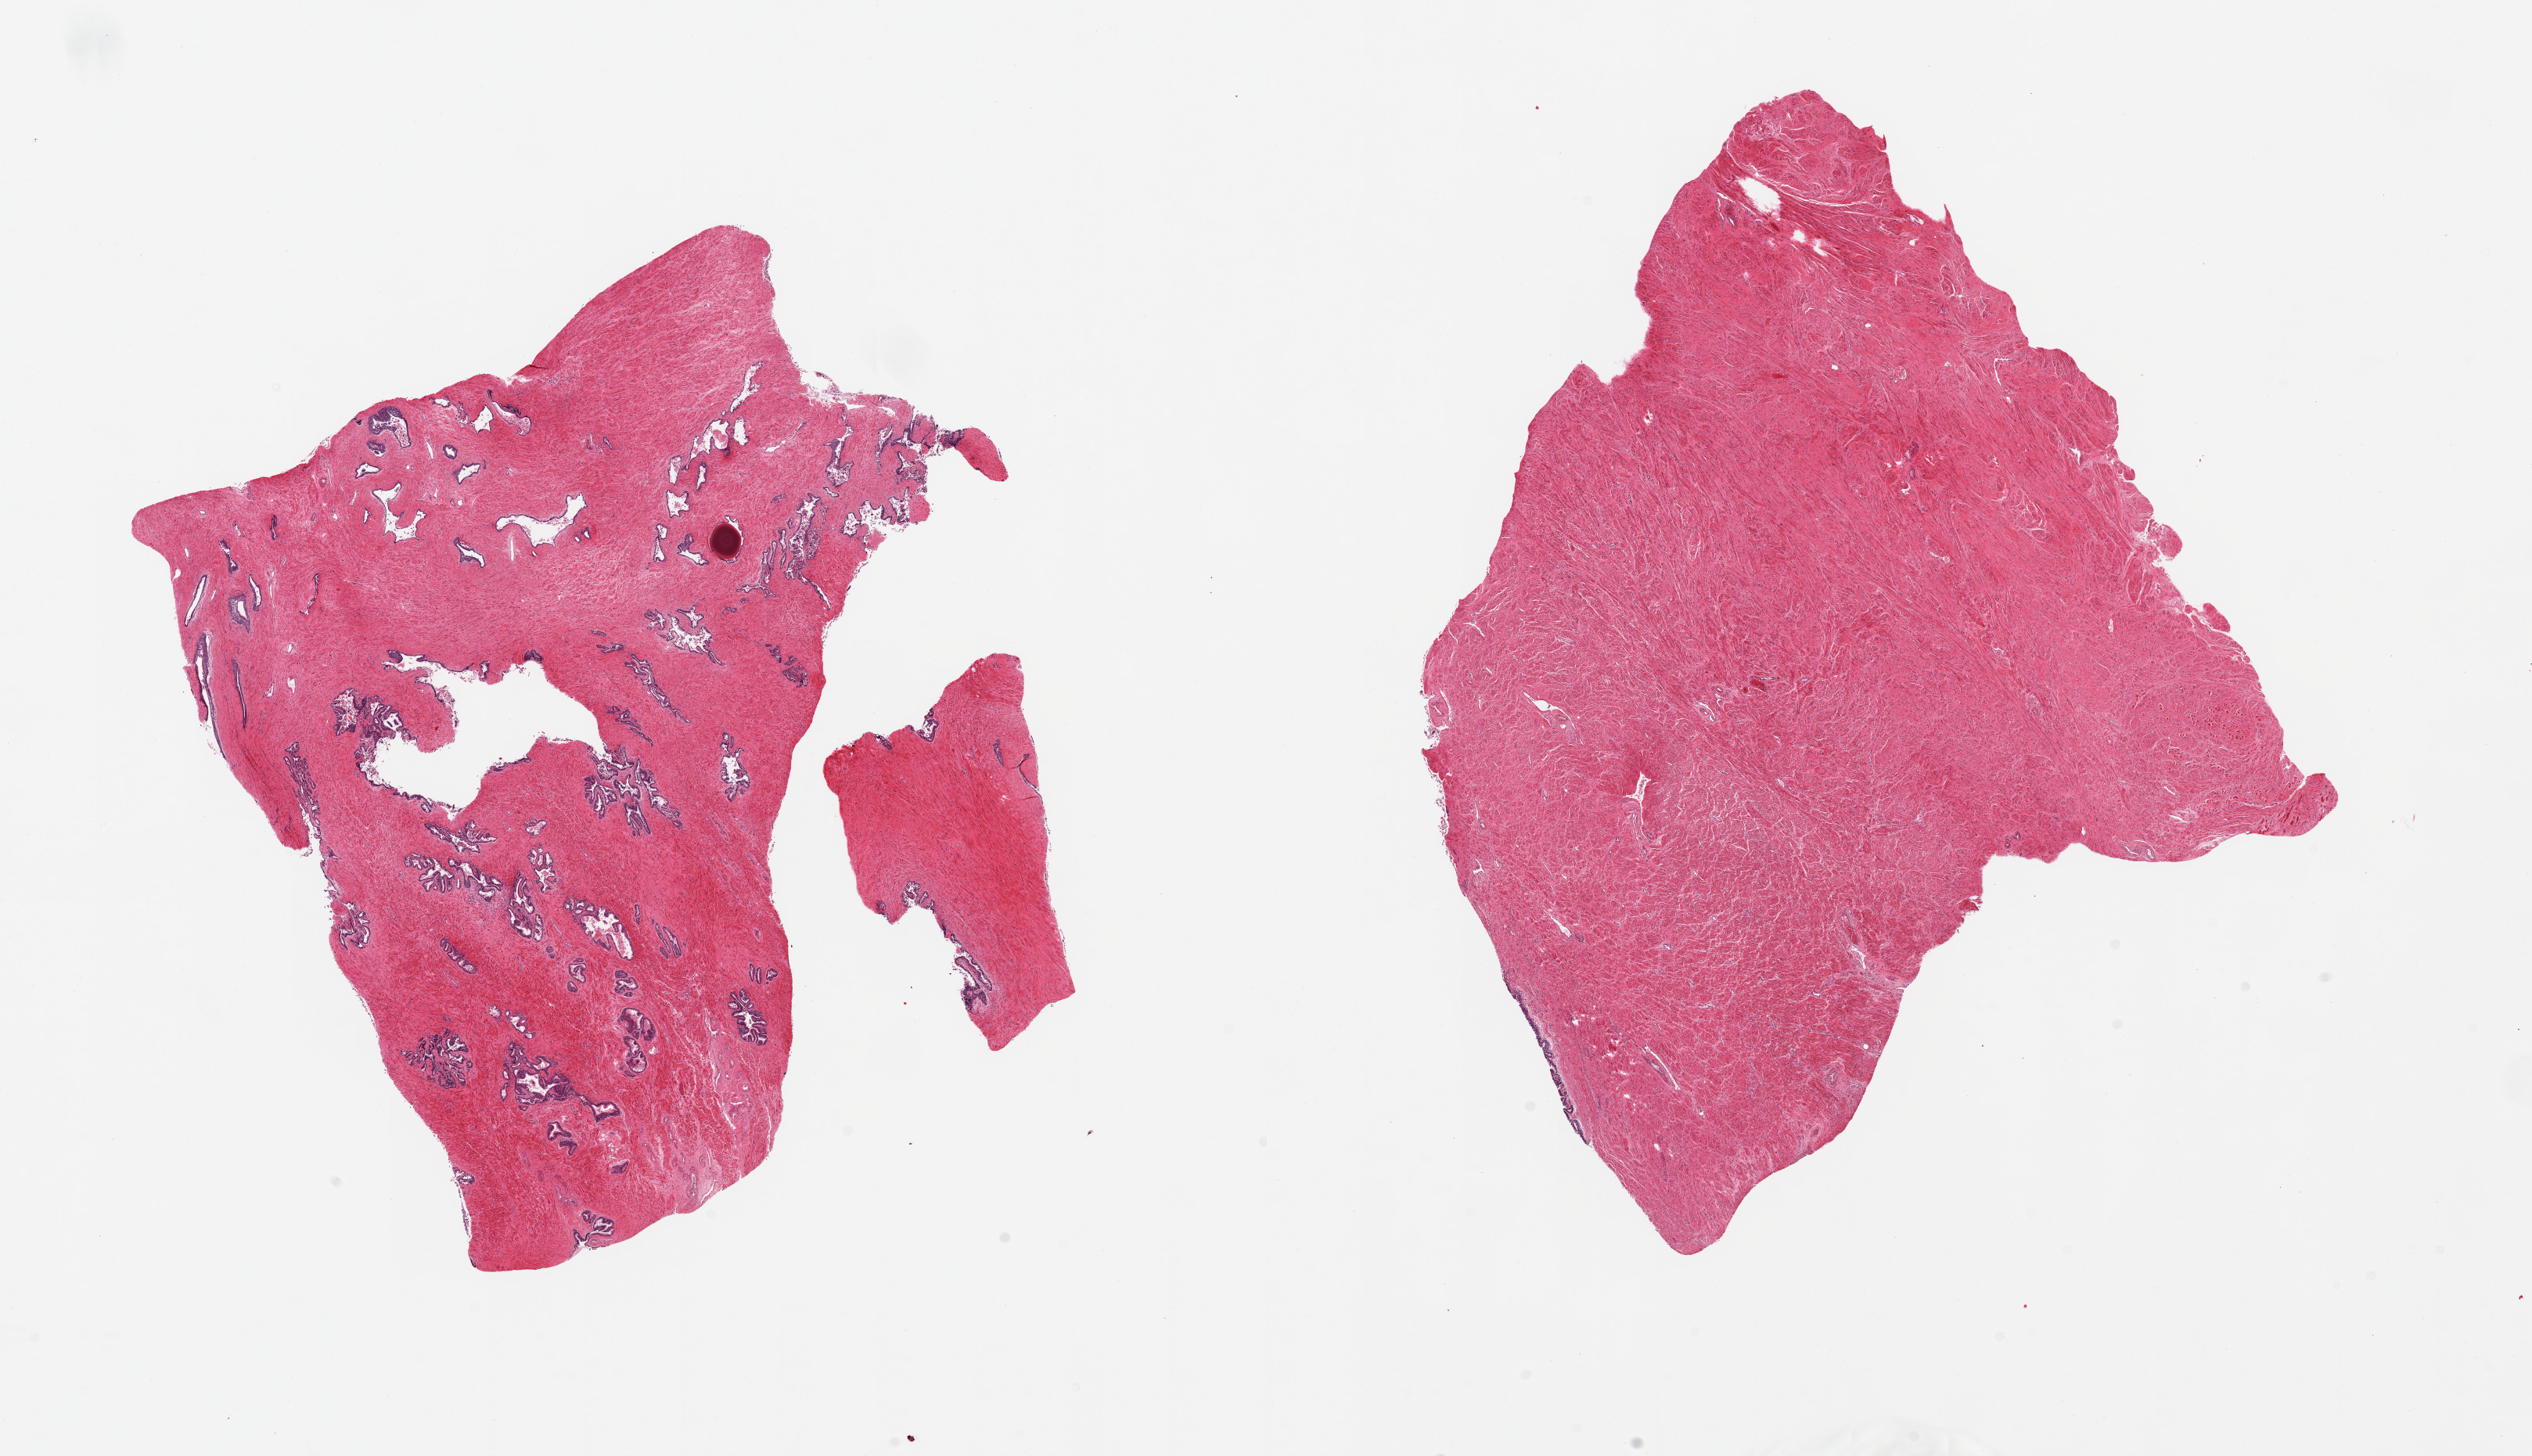
Digitized haematoxylin and eosin-stained section, brightfield — low-resolution overview of the scanned area, about 25.6 x 14.7 mm. PAXgene-fixed paraffin-embedded (PFPE) section. Section of prostate (target tissue). Donor tissue sample. Donor sex: male.
• pathologist's review note for this sample: 3 pieces; portion of prostatic urethra, one consists of fibromuscular stroma and focal skeletal muscle, others with glandular component embedded in fibromuscular stroma